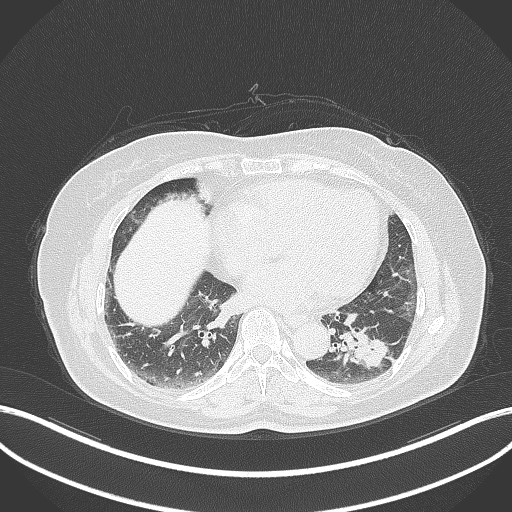
Chest CT, one axial slice. Position 143 of 311 along the scan axis. Lung window (W 1500 / L -600 HU). 512 × 512 image matrix, field of view 400 × 400 mm. Female patient, age 59 years. Case-level facts recorded for this patient, not image findings: clinical TNM (as recorded): T2a N0 M0; histopathological grade: G2-3.
Annotated regions visible in this slice (rectangle marked by the reading radiologist):
- lung tumour (recorded histology: adenocarcinoma): bounding box <338,326,392,374> (left, top, right, bottom; pixels)